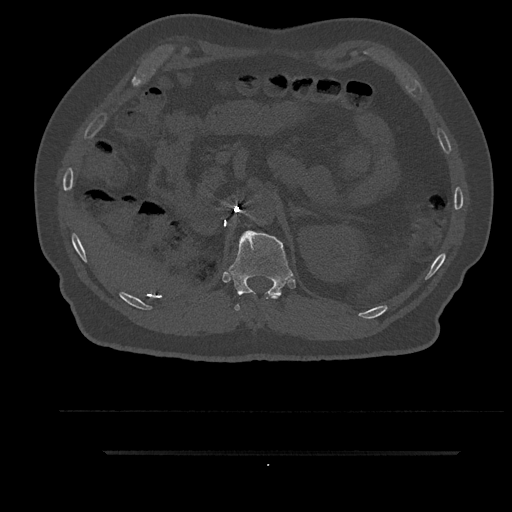
CT including the spine, one axial slice. Position 258 of 797 along the scan axis. Reconstruction kernel Br40s/3. Bone window (W 1800 / L 400 HU). 512 × 512 image matrix, field of view 432 × 432 mm. Patient: male, 63 years. Case-level facts recorded for this patient, not image findings: primary cancer: renal; vertebrae with lytic lesions (as recorded): T8.
Structures marked on this image (semi-automatically segmented with operator editing):
- T11 vertebra: box from (x=266, y=295) to (x=279, y=299) px
- T12 vertebra: (x=227, y=230)–(x=294, y=311)